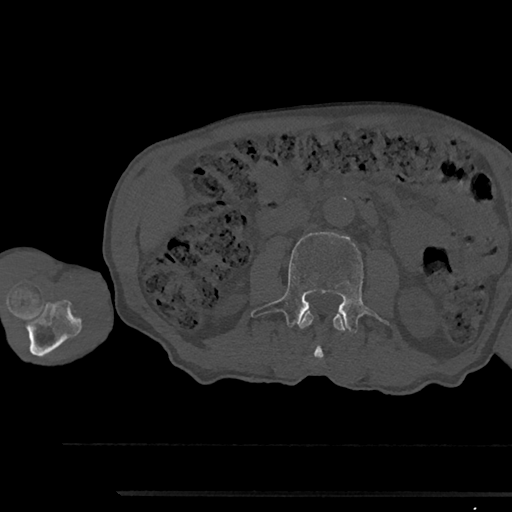
CT including the spine, one axial slice; slice 510 of 797 in the series (ordered by position); reconstruction kernel Br40s/3; 120 kVp; bone window (W 1800 / L 400 HU); 512 × 512 image matrix. Patient: male, 79 years. From the clinical record (not read from this slice): primary cancer: prostate.
Outlined on this slice (semi-automatically segmented with operator editing):
- L2 vertebra: bounding box <298,312,347,360> (left, top, right, bottom; pixels)
- L3 vertebra: <251,232,390,332>